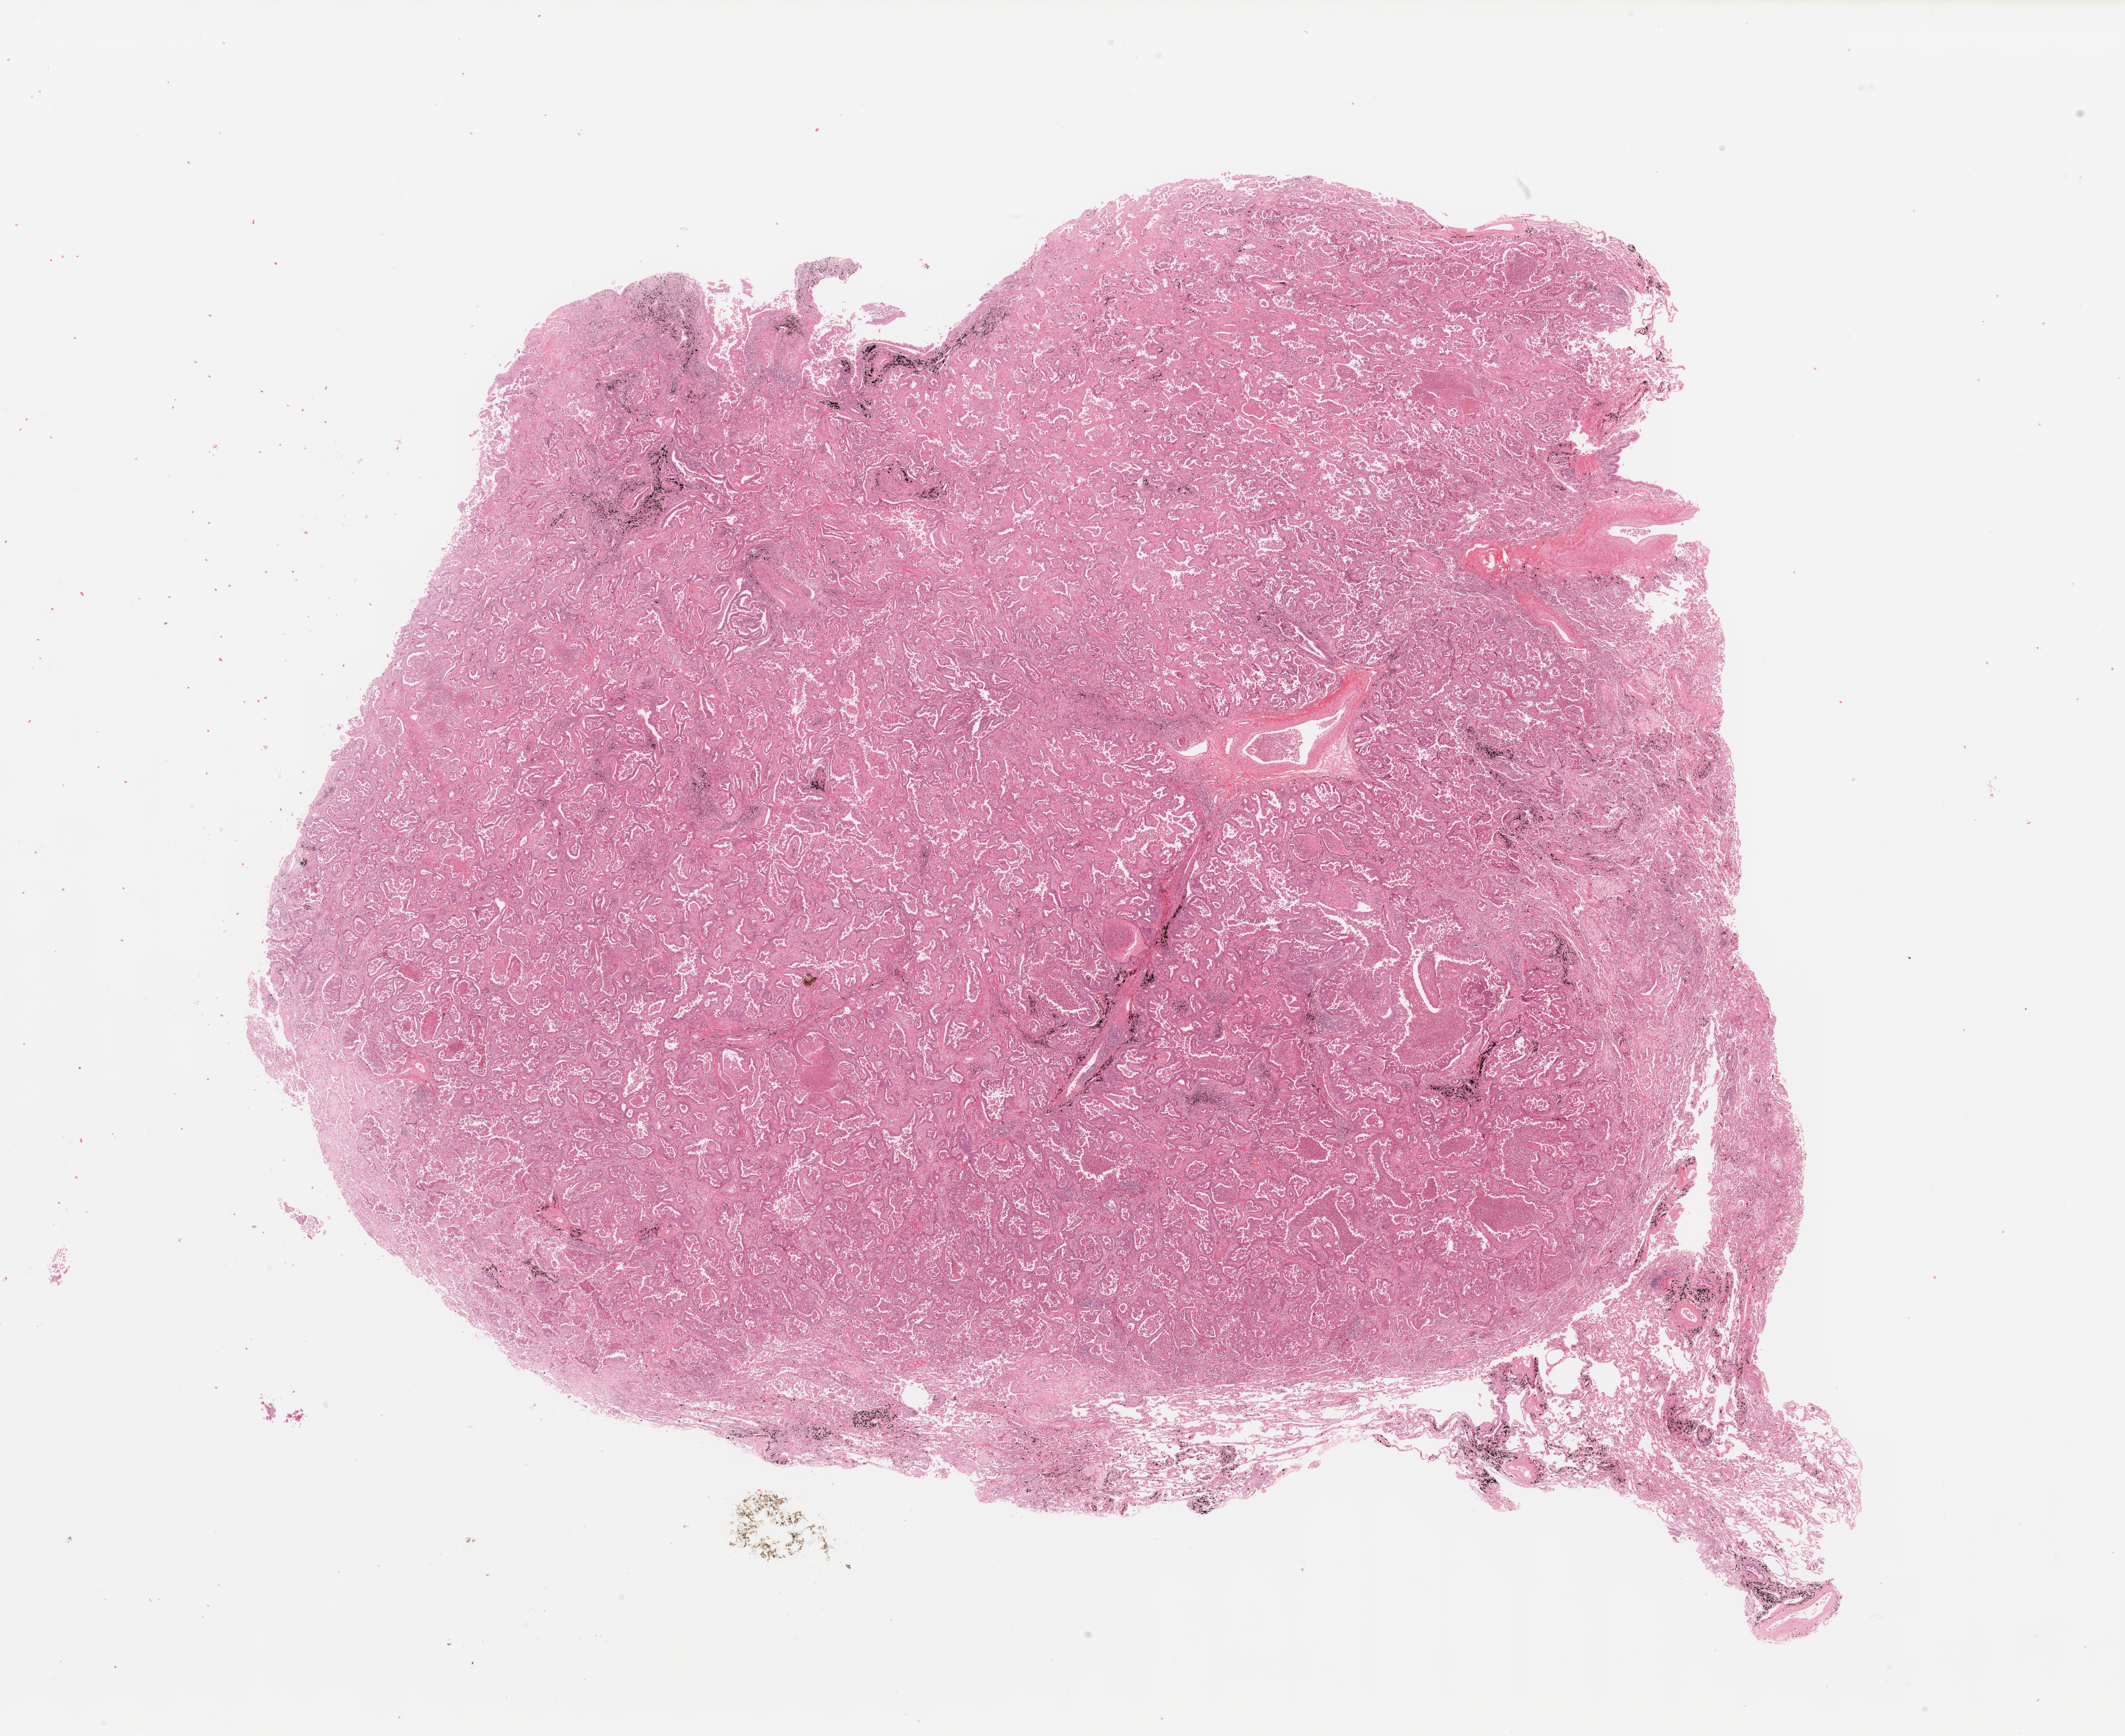
Digitized H&E tissue section (whole slide), a low-resolution overview of the entire scanned area, about 27.6 x 22.5 mm (slide scanned at 20x). Tumour tissue sample, sampled site: lung. 69-year-old male patient. Histologic grade: G2 (moderately differentiated). Composition of this section per pathologist review: tumour nuclei 75%, necrosis 5%.
• primary tumour site (as recorded): left lower lobe
• diagnosis: Adenocarcinoma, NOS
• AJCC pathologic stage: IB